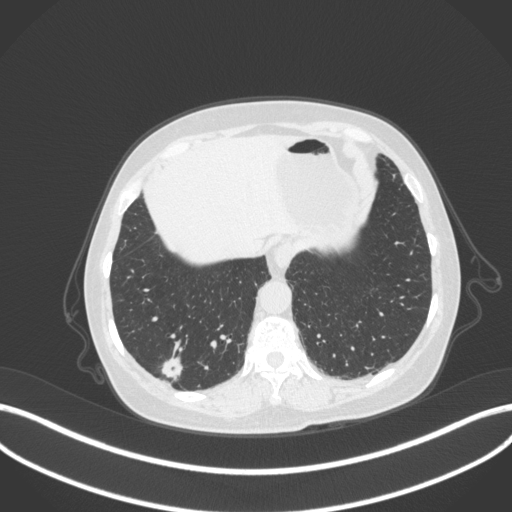
Chest CT, one axial slice; slice 57 of 340 in the series (ordered by position); lung window (W 1500 / L -600 HU); 512 × 512 image matrix, field of view 400 × 400 mm. Female patient, age 69 years. From the clinical record (not read from this slice): clinical TNM (as recorded): T1b N0 M0; histopathological grade: G2-3.
Annotated regions visible in this slice (rectangle marked by the reading radiologist):
- lung tumour (recorded histology: adenocarcinoma): box from (x=156, y=353) to (x=188, y=384) px